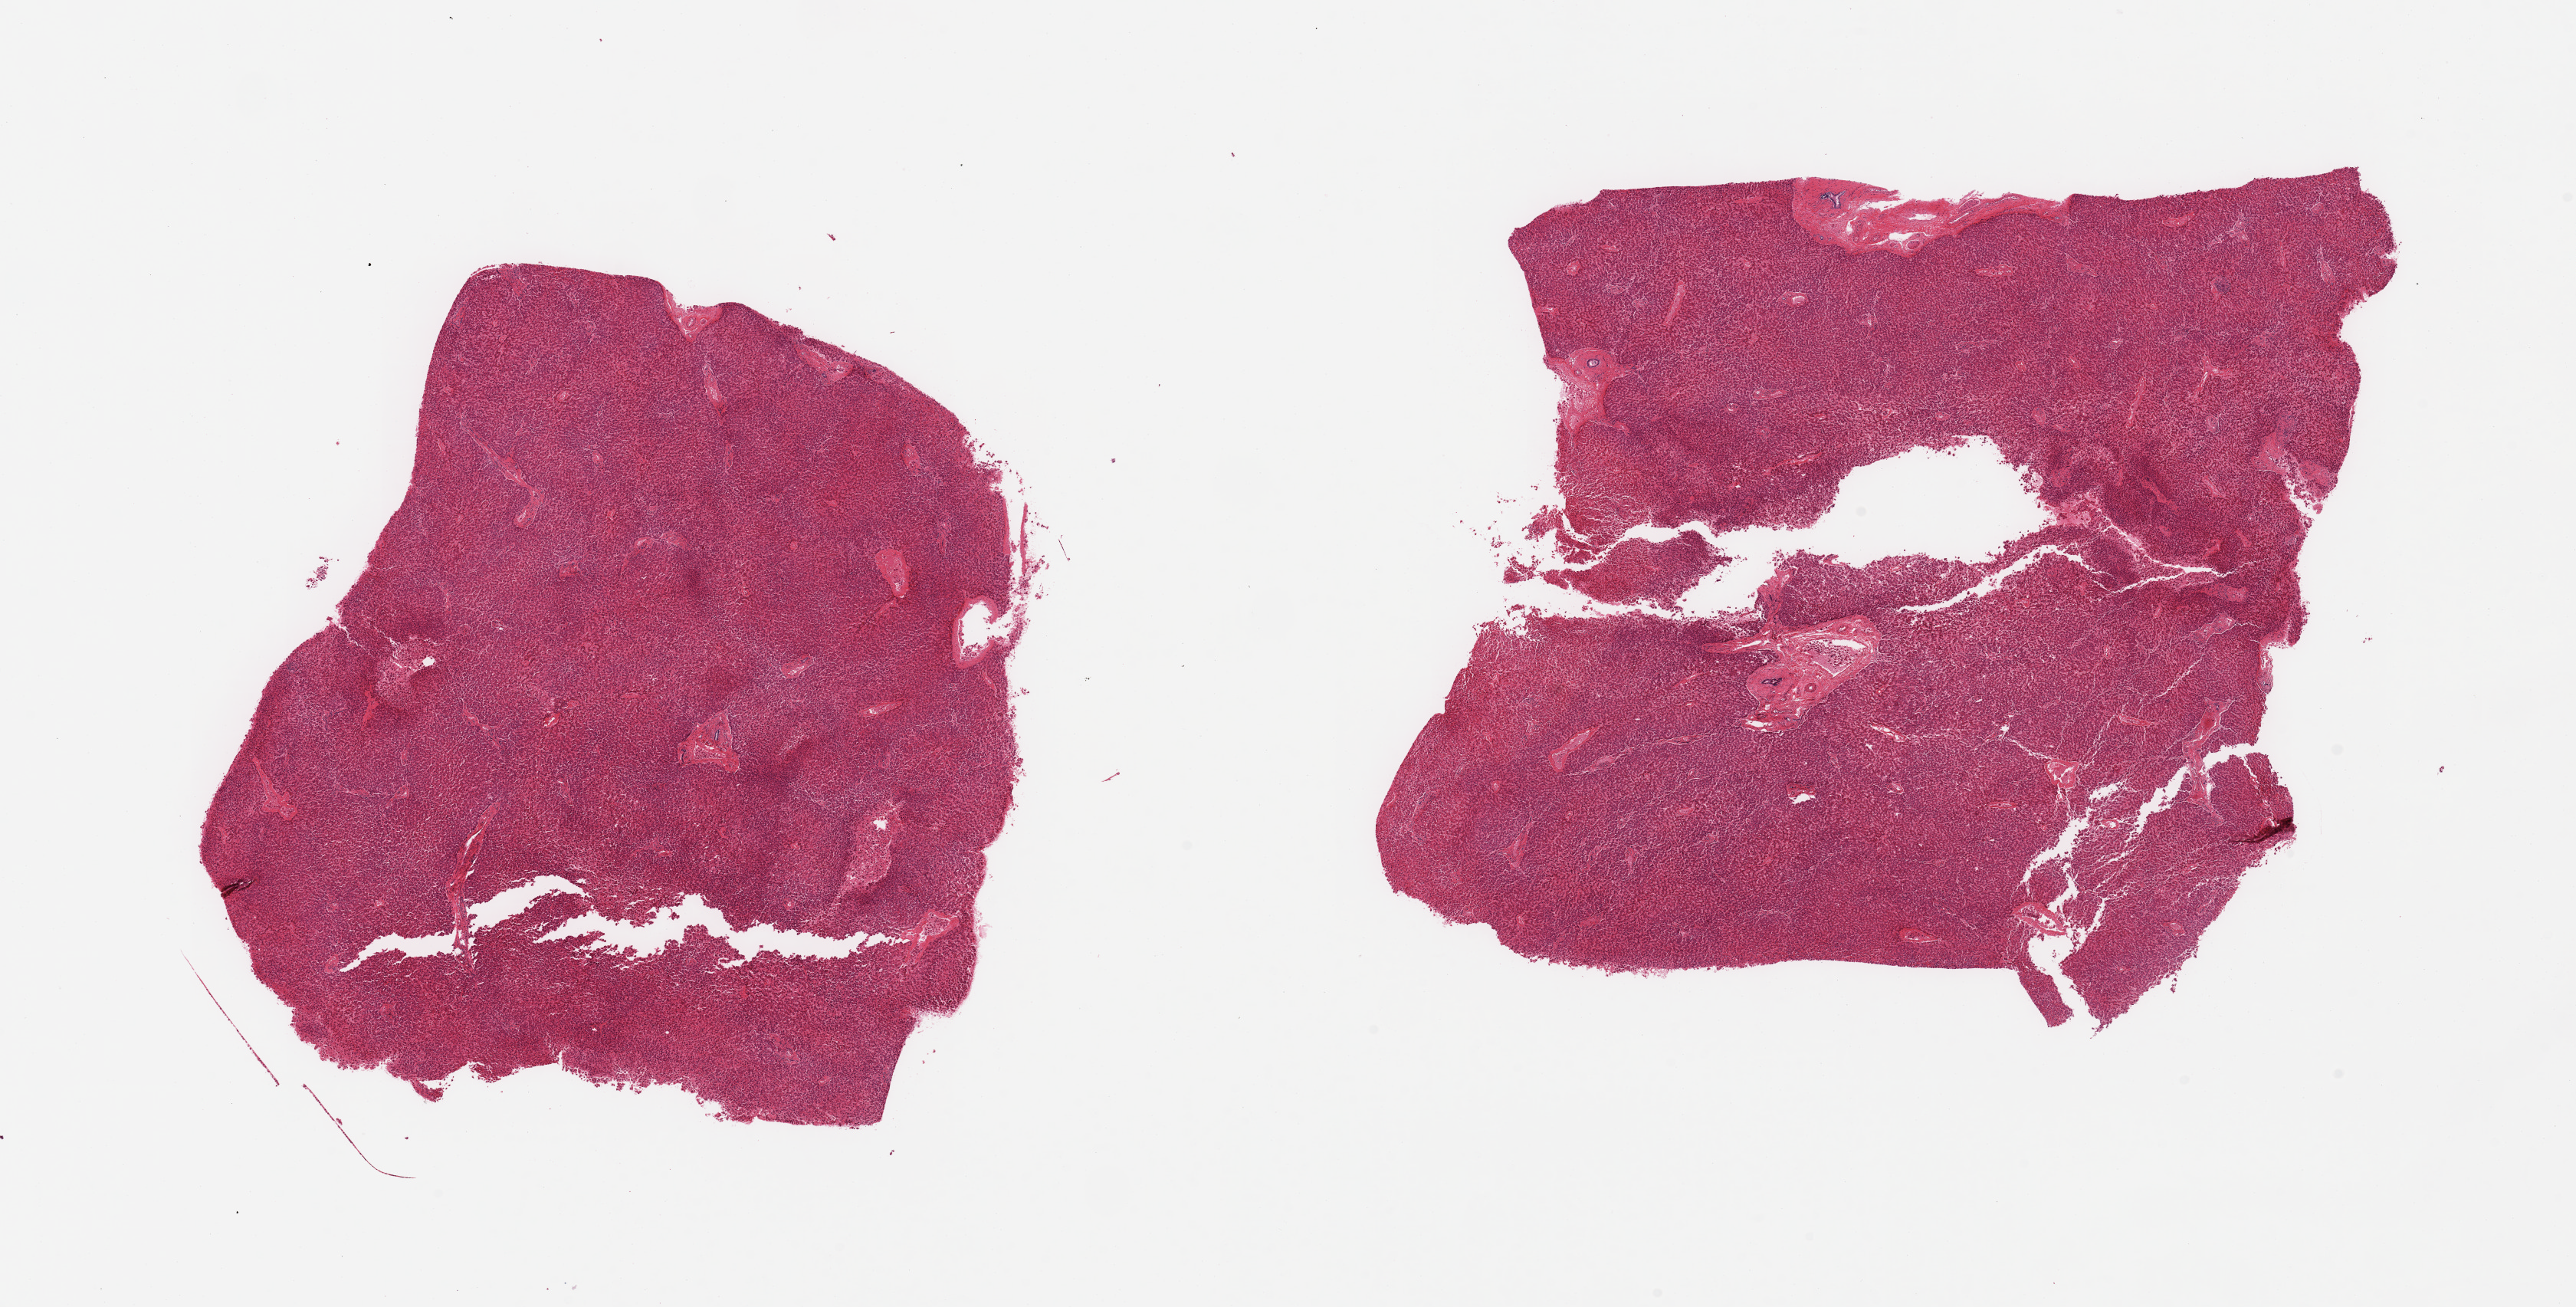
Haematoxylin and eosin whole-slide image — a low-resolution overview of the entire scanned area, about 26.6 x 13.5 mm. PAXgene-fixed, paraffin-embedded tissue. Sampled site (target tissue): liver. Tissue donor sample.
* pathologist's review note for this sample: 2 pieces